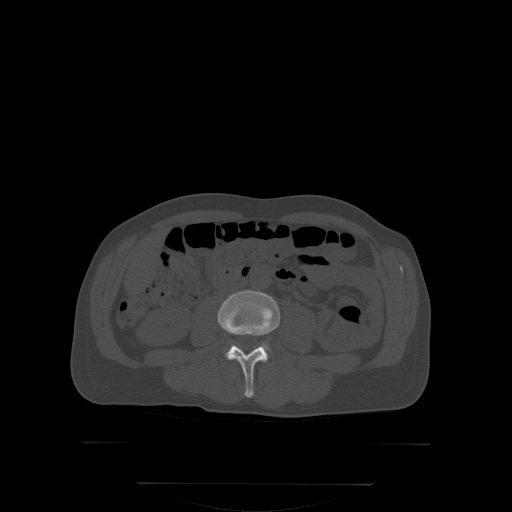
CT including the spine, one axial slice. Slice 119 of 350 in the series (ordered by position). Bone window (W 1800 / L 400 HU). 512 × 512 image matrix. Patient: male, 58 years. Case-level facts recorded for this patient, not image findings: primary cancer: prostate.
Outlined on this slice (semi-automatic segmentation, software-assisted and operator-edited):
- L3 vertebra: box from (x=219, y=291) to (x=280, y=396) px
- L4 vertebra: (x=262, y=343)–(x=272, y=353)